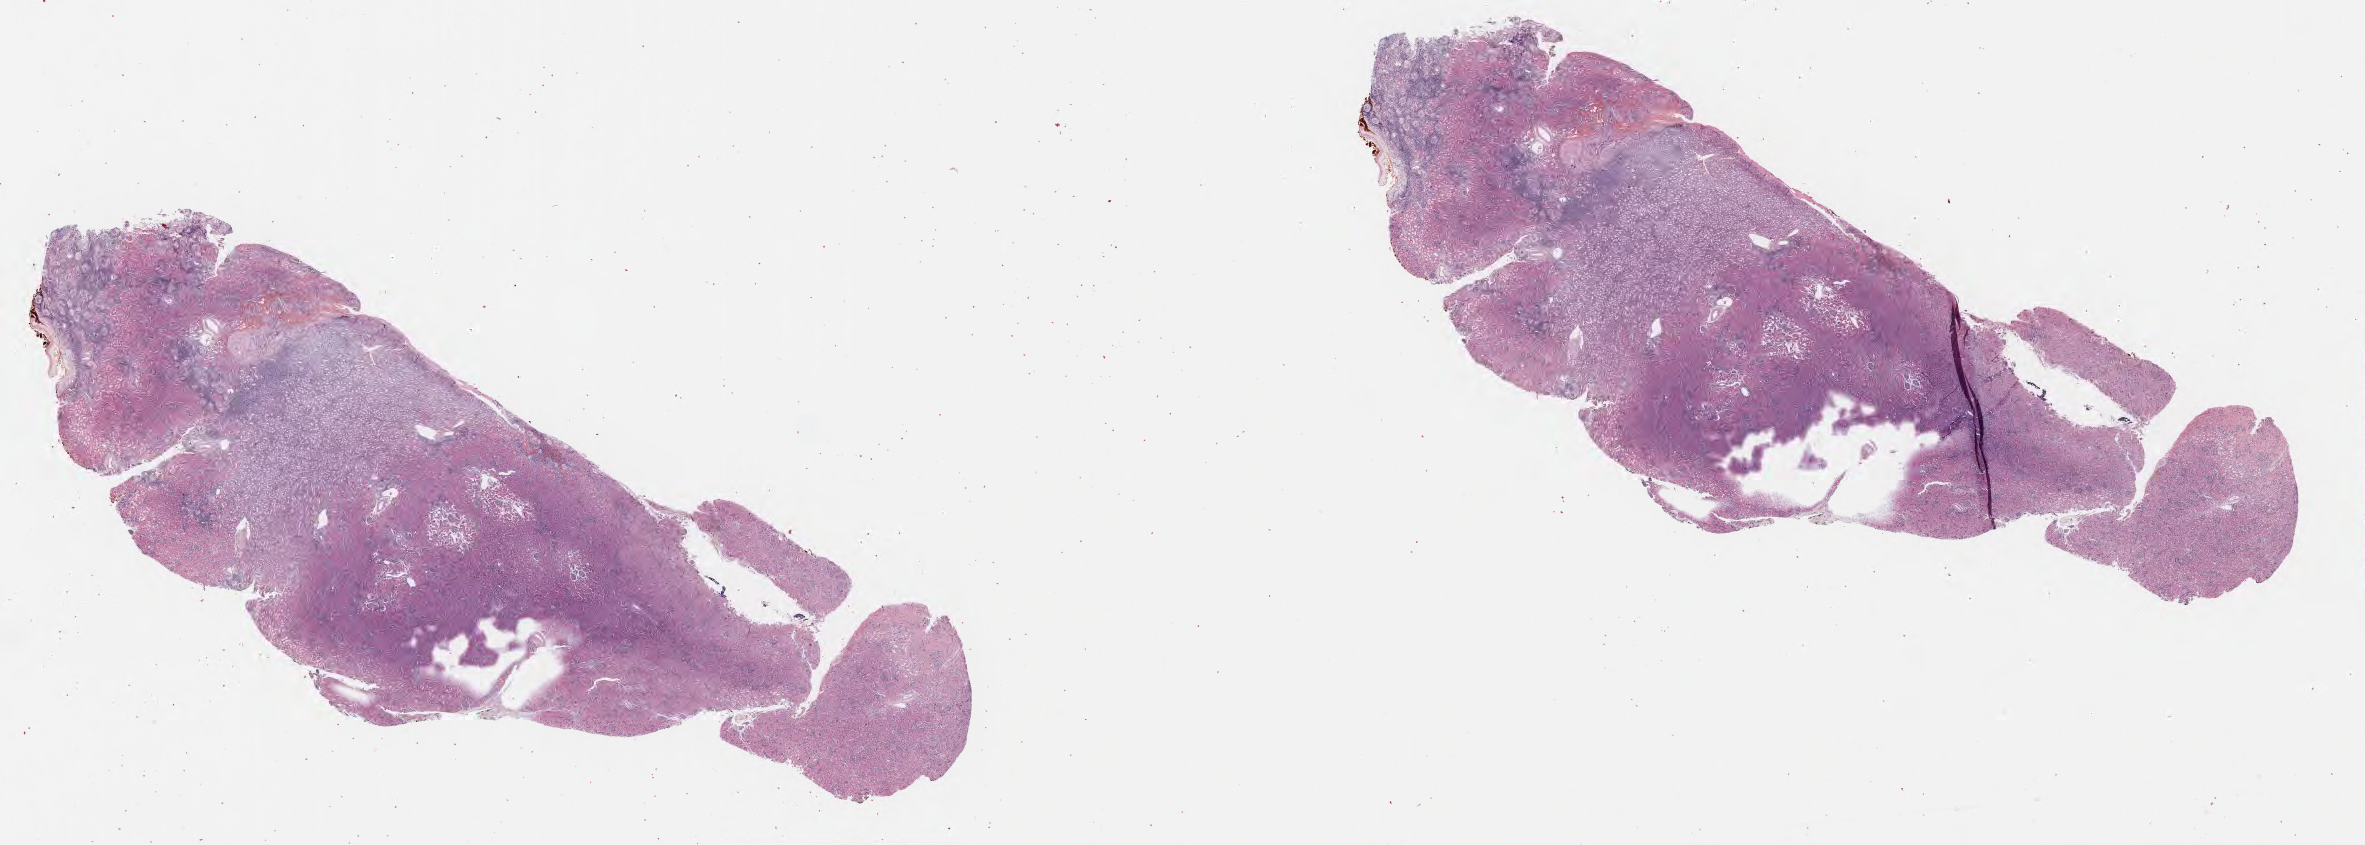
Whole-slide image, haematoxylin and eosin stain, whole scanned area (about 38.3 x 13.7 mm) shown as a low-resolution overview. FFPE section. Specimen: normal-tissue sample (non-tumor) from a patient with nephroblastoma, NOS. Site: kidney. Female patient; age at initial diagnosis 3 years. Pathologist review of this section (percent, as recorded): tumor cells 0%, tumor nuclei 0%, stromal cells 20%, necrosis 0%, normal cells 80%. Inflammatory infiltration, as recorded: lymphocyte infiltration 30%, monocyte infiltration 2%, neutrophil infiltration 0%.
This section: non-tumor tissue sample; the patient's diagnosis is given above.